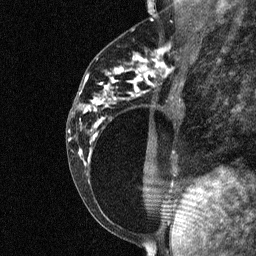
Breast MRI (dynamic contrast-enhanced), one sagittal slice. Dynamic contrast-enhanced study with each time point stored as its own series, time point 2 of 3 at this slice position (early post-contrast, ordered by acquisition time). 1.5 T. TE 4.8 ms, TR 27 ms. 2 mm slice thickness. 256 × 256 image matrix. Patient: female, 34 years. Case-level facts recorded for this patient, not image findings: setting: breast cancer imaged before/during neoadjuvant chemotherapy; receptor status: HR-positive, HER2-negative.
Outlined on this slice (semi-automatic segmentation, software-assisted and operator-edited):
- analysis volume of interest (the breast-tissue region the enhancement analysis was run in; not a lesion): box from (x=78, y=44) to (x=181, y=191) px
- tumour enhancement mask (voxels above the 90 % enhancement threshold inside the analysis volume of interest): (x=157, y=49)–(x=164, y=66)